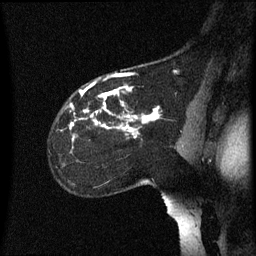
Breast MRI (dynamic contrast-enhanced), one sagittal slice. Position 43 of 60 along the scan axis. Dynamic contrast-enhanced series, image 2 of 3 at this slice position (ordered by acquisition). 1.5 T. TE 4.2 ms, TR 8.4 ms. 2.2 mm slice thickness. 256 × 256 image matrix. Patient: female, 35 years. From the clinical record (not read from this slice): setting: breast cancer imaged before/during neoadjuvant chemotherapy; receptor status: HER2-positive.
Outlined on this slice (semi-automatically segmented with operator editing):
- analysis volume of interest (the breast-tissue region the enhancement analysis was run in; not a lesion): bounding box [x1, y1, x2, y2] px = [50, 72, 178, 167]
- tumour enhancement mask (voxels above the 70 % enhancement threshold inside the analysis volume of interest): [70, 74, 160, 137]